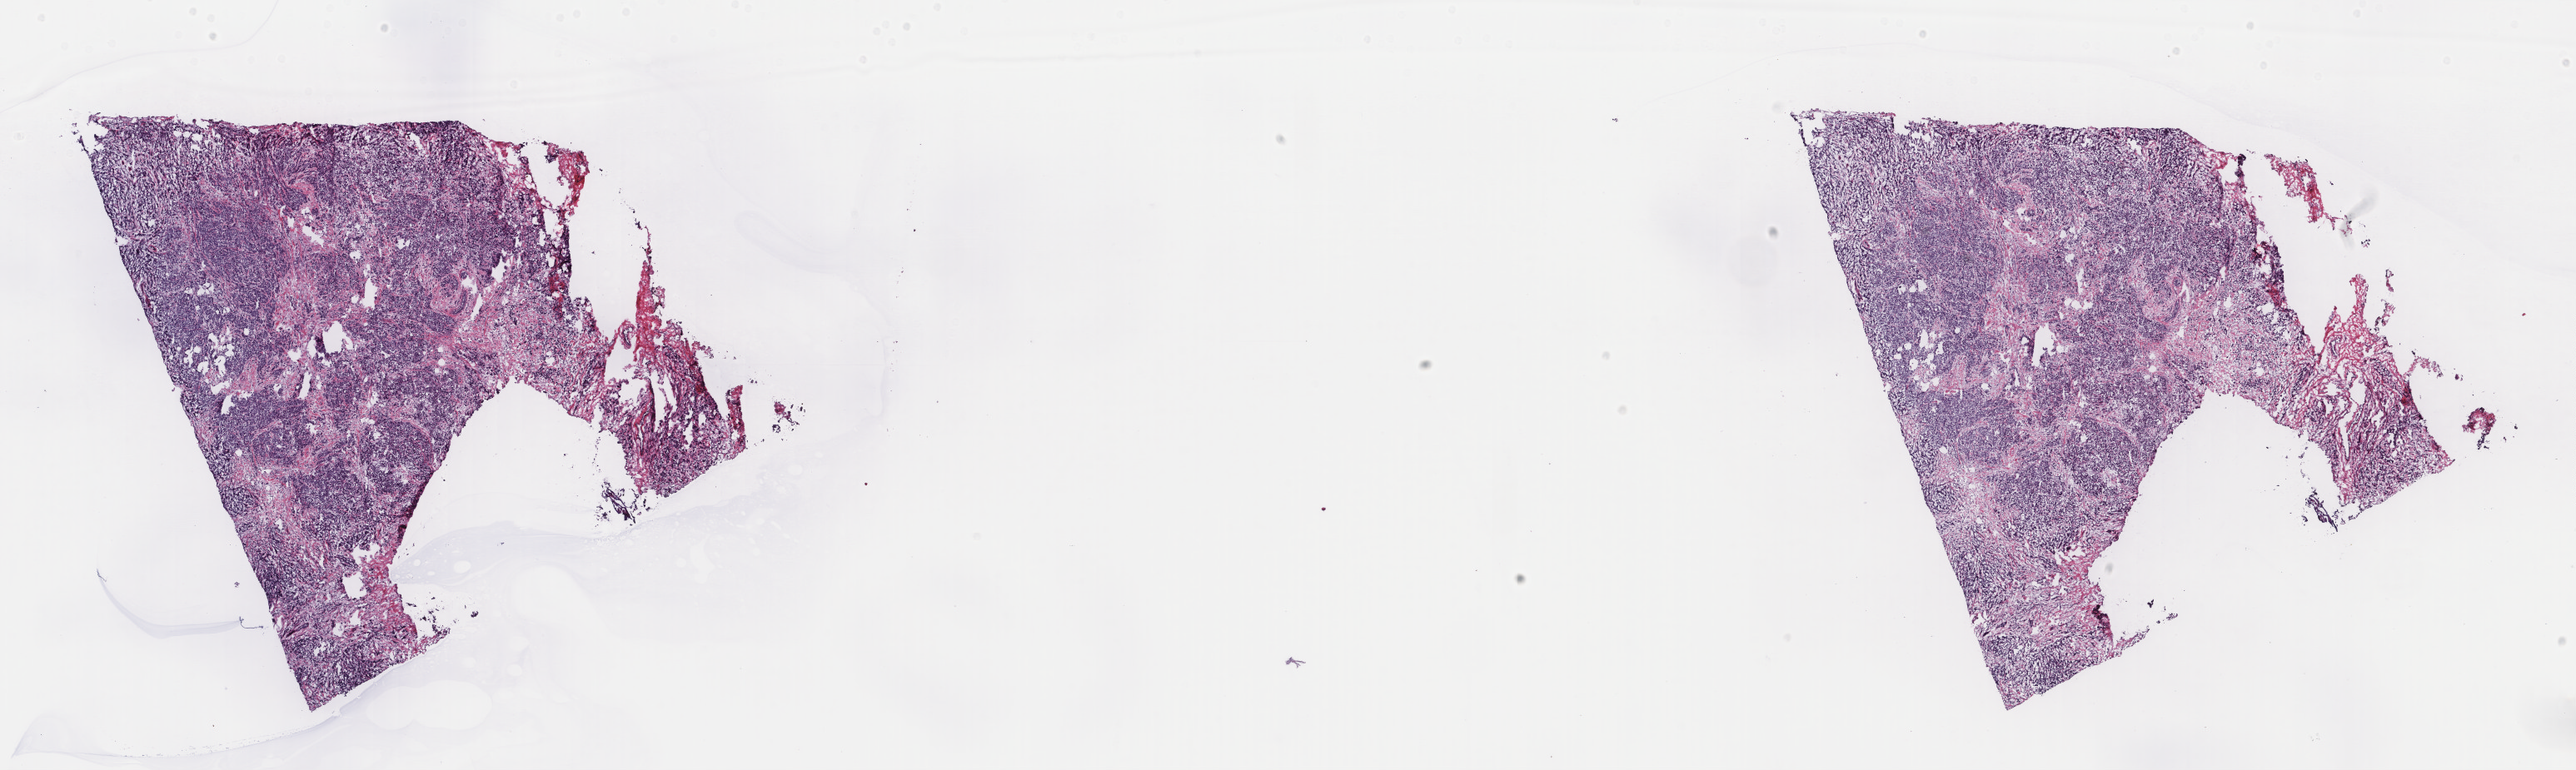
H&E-stained whole-slide image, low-resolution overview of the scanned area, about 24.6 x 7.3 mm, frozen section from the top of the tissue portion, sample: primary tumour, breast. Female, age 69 years at initial diagnosis. Slide review estimates, as recorded: tumour cells 80%, tumour nuclei 90%, normal cells 0%, stromal cells 20%, necrosis 0%. Inflammatory infiltration, as recorded: lymphocyte infiltration 0%, monocyte infiltration 0%, neutrophil infiltration 0%.
- laterality: left
- AJCC pathologic stage: IIA (7th edition)
- lymph nodes positive (case pathology): 0 of 5 examined
- histologic diagnosis: Lobular carcinoma, NOS